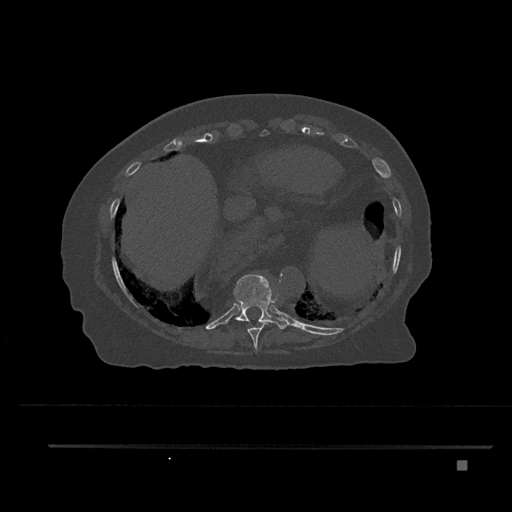
CT including the spine, one axial slice; position 373 of 797 along the scan axis; reconstruction kernel Br40s/3; 120 kVp; bone window (W 1800 / L 400 HU); 512 × 512 image matrix, field of view 437 × 437 mm. Patient: female, 76 years. Case-level facts recorded for this patient, not image findings: primary cancer: lung; vertebrae with lytic lesions (as recorded): T11, L3.
Structures marked on this image (semi-automatically segmented with operator editing):
- T10 vertebra: bounding box <226,274,290,329> (left, top, right, bottom; pixels)
- T9 vertebra: <241,320,268,350>